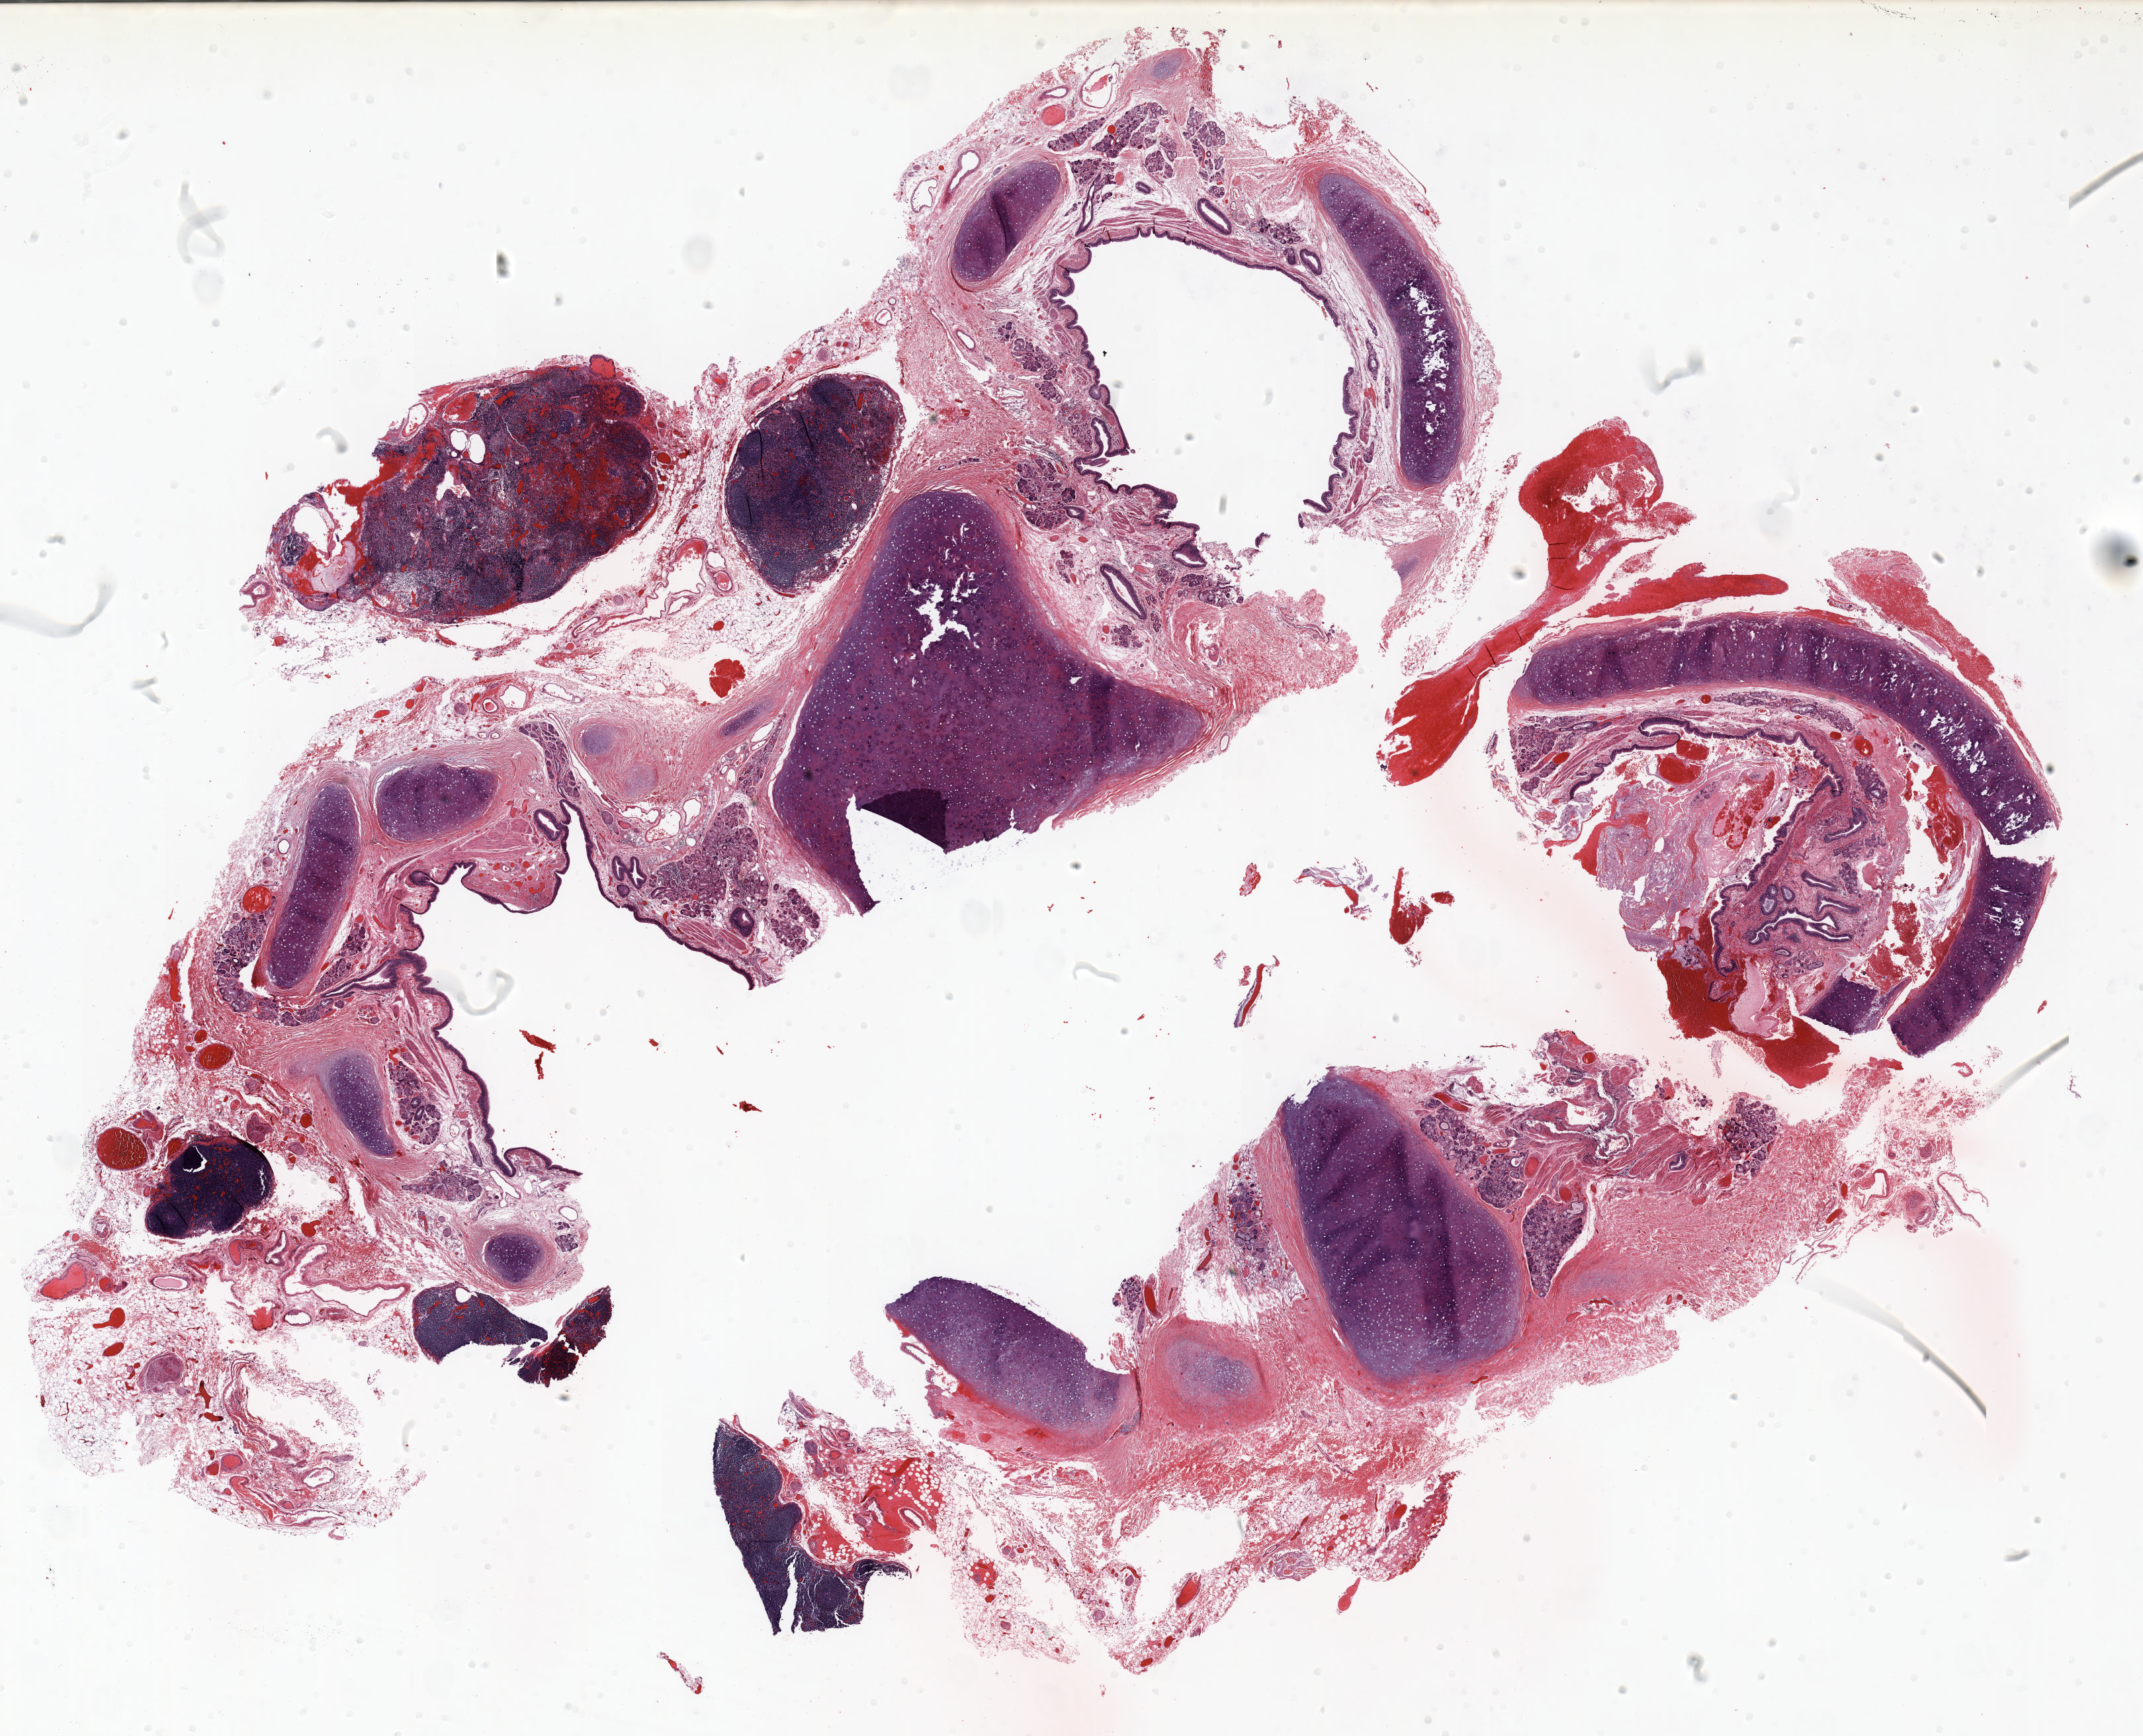
H&E-stained whole-slide image, a low-resolution overview of the entire scanned area, about 26.0 x 21.1 mm, FFPE section, lung tissue. Female, age 57 at enrolment. Former smoker at enrolment. Grade: moderately differentiated (G2).
• primary tumour location (clinical record): left upper lobe
• participant's lung-cancer diagnosis: Adenocarcinoma with mixed subtypes (ICD-O-3 8255/3)
• stage (AJCC 6th edition): IIIB
• ICD-O-3 topography: upper lobe of lung (C34.1)
• tumour size (pathology): 19 mm